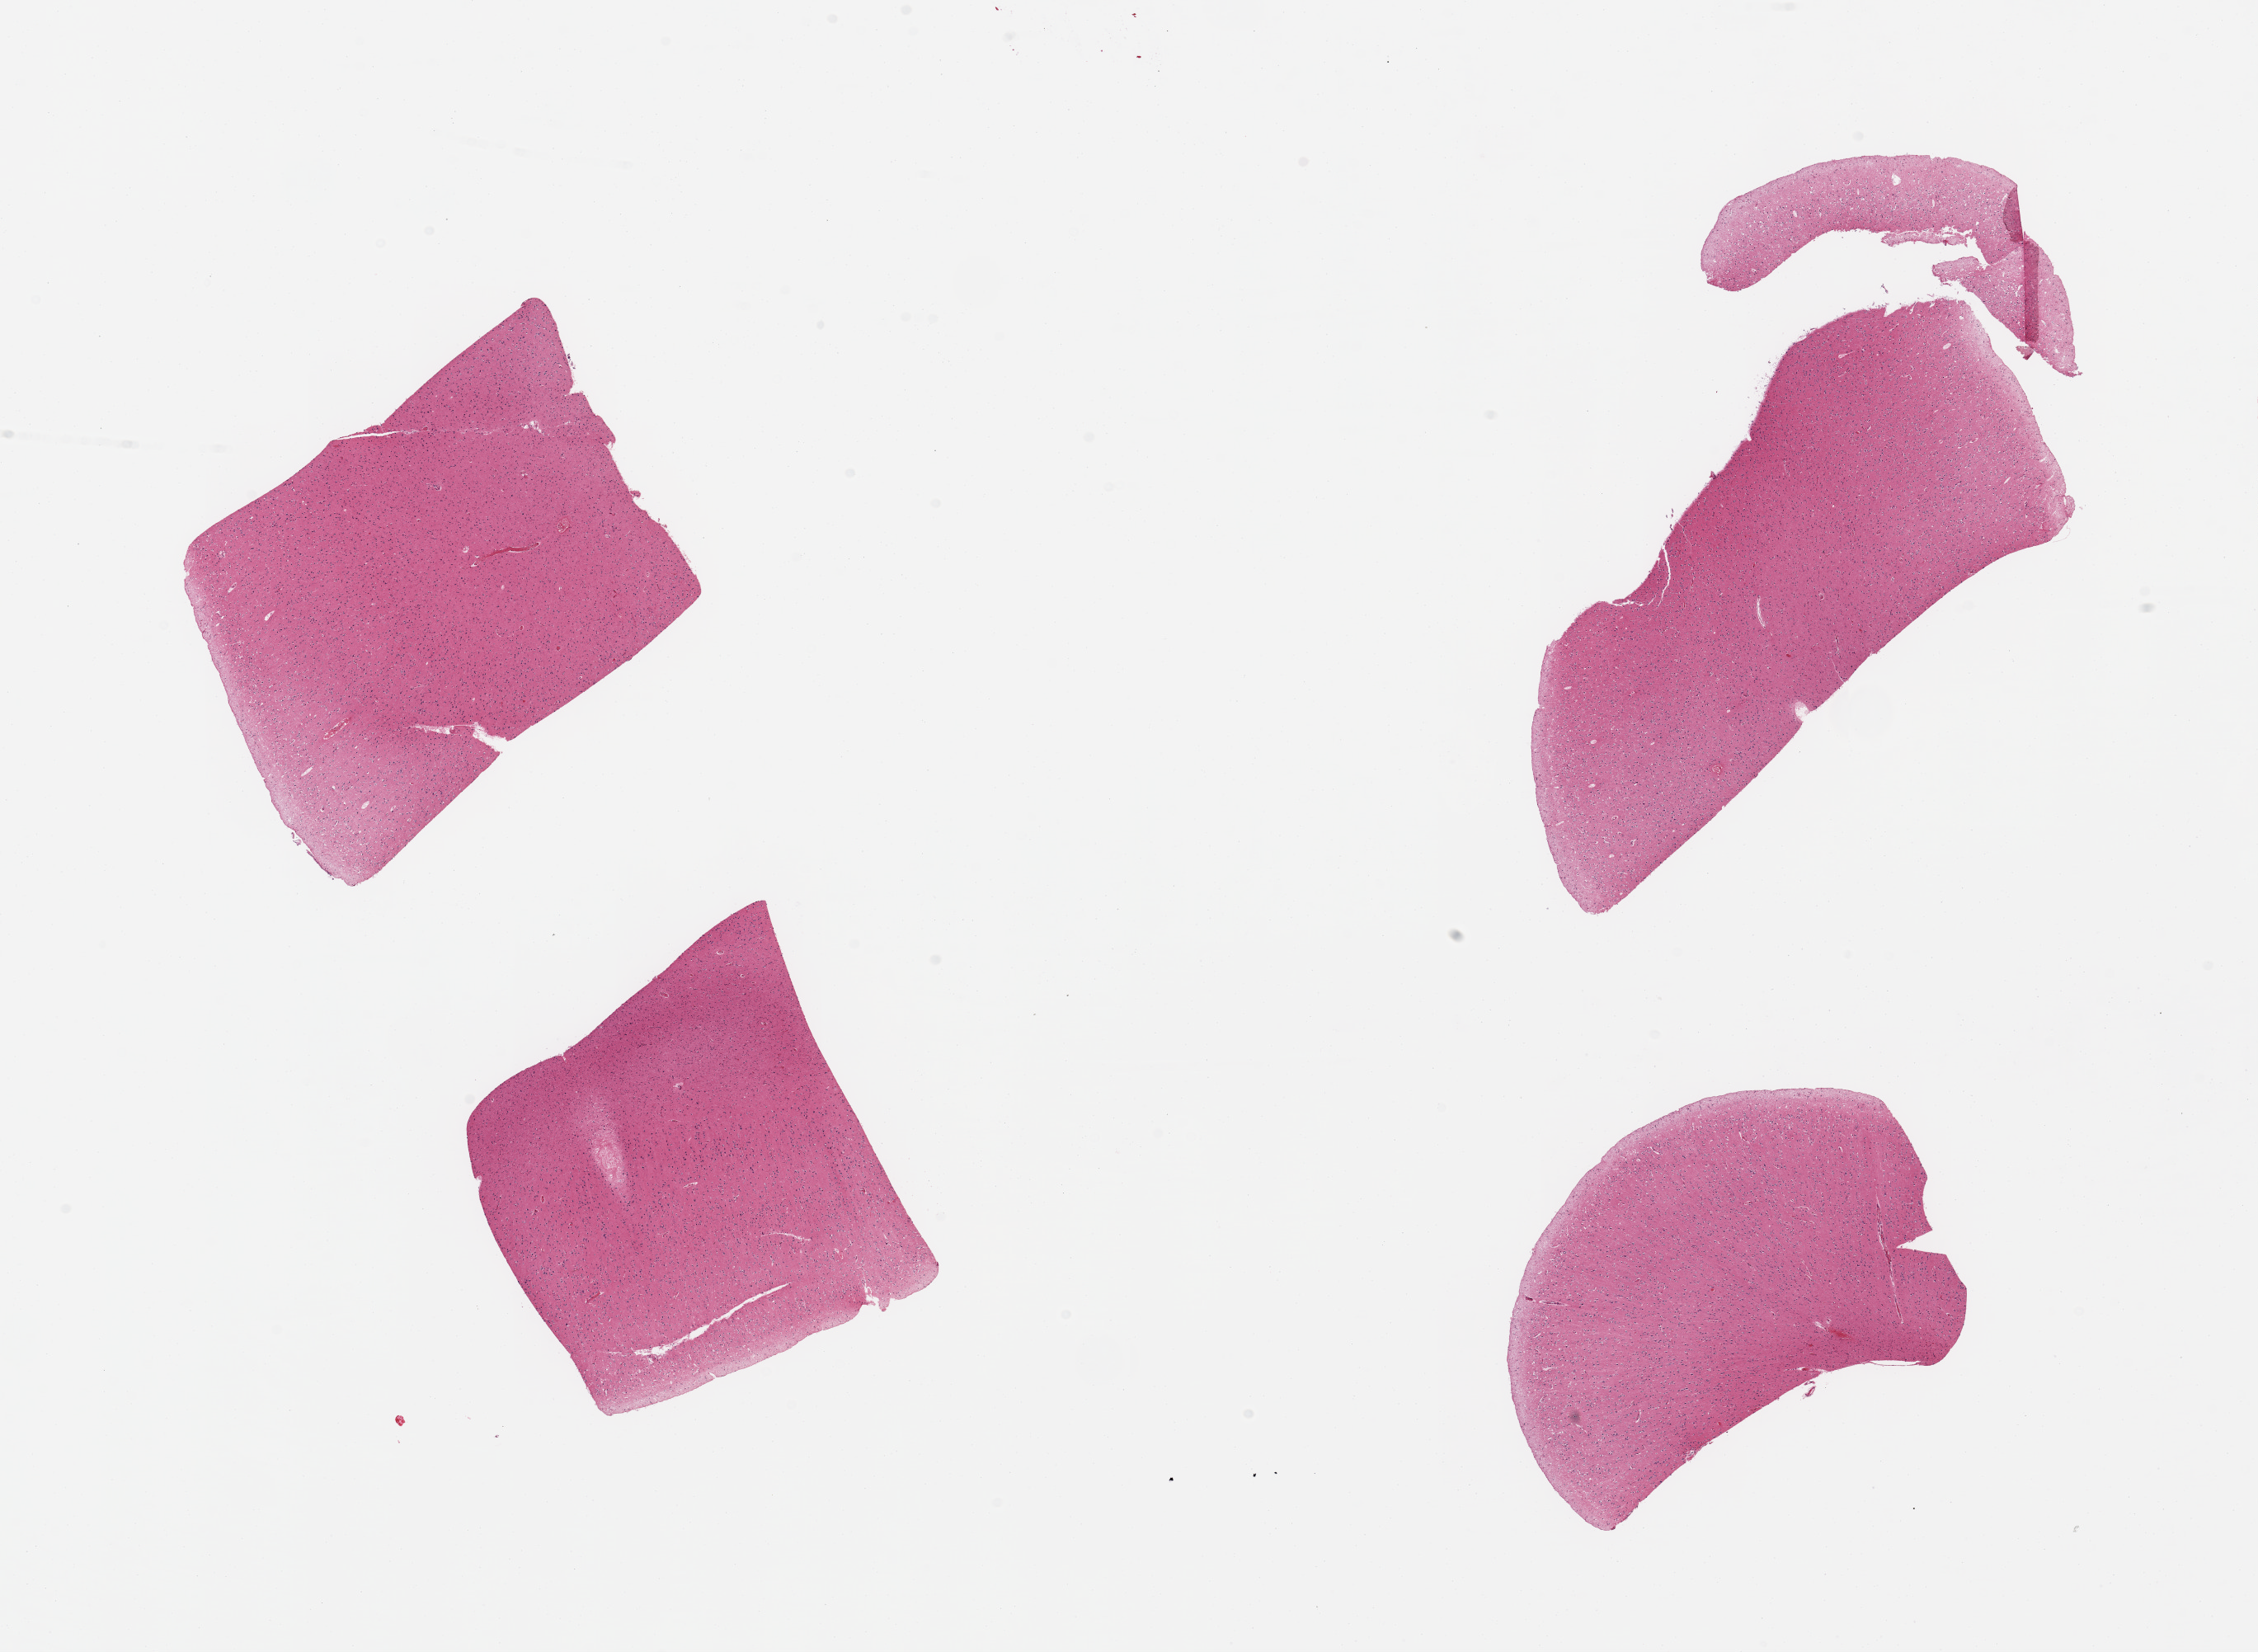
H&E whole-slide image, shown as a low-resolution overview of the whole scanned area (about 21.7 x 15.8 mm); PAXgene-fixed, paraffin-embedded tissue; section of cerebral cortex (target tissue); donor tissue sample. Donor sex: female.
Review note (as recorded): 4 pieces.